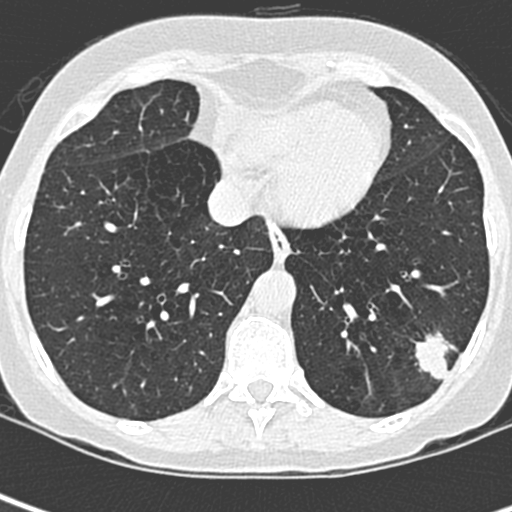
Low-dose screening chest CT, one axial slice; slice 89 of 252 in the series (ordered by position); 120 kVp; lung window (W 1500 / L -600 HU); 1.3 mm slice thickness; 512 × 512 image matrix, field of view 271 × 271 mm.
Annotated regions visible in this slice (manually delineated by an expert):
- lesion 1 (tumor, lower lobe of left lung): bounding box [x1, y1, x2, y2] px = [415, 334, 449, 381]